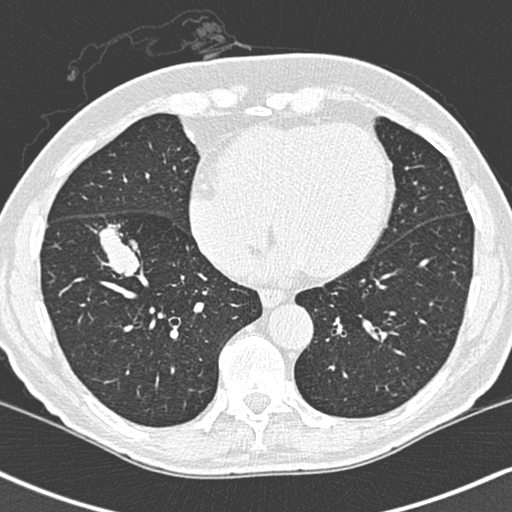
Low-dose screening chest CT, one axial slice; slice 98 of 248 in the series (ordered by position); 120 kVp; lung window (W 1500 / L -600 HU); 1.3 mm slice thickness; 512 × 512 image matrix.
Outlined on this slice (outlined manually by an expert reader):
- lesion 1 (tumor, lower lobe of right lung): bounding box (x1, y1, x2, y2) in pixels: (99, 186, 140, 239)